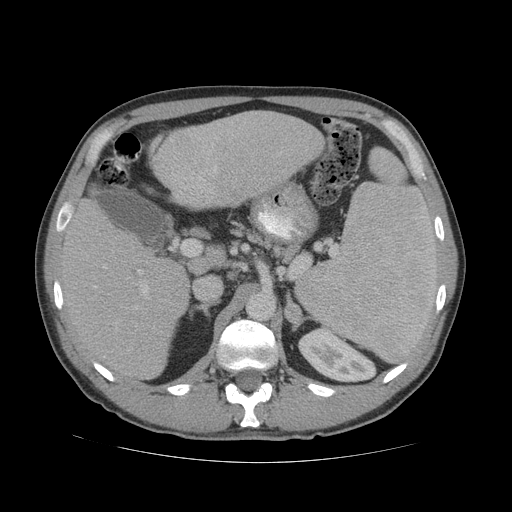
Contrast-enhanced abdominal CT (liver protocol), one axial slice; slice 35 of 81 in the series (ordered by position); reconstruction kernel STANDARD; 140 kVp; soft-tissue window (W 400 / L 40 HU); 2.5 mm slice thickness; 512 × 512 image matrix. Case-level facts recorded for this patient, not image findings: diagnosis: hepatocellular carcinoma (patient treated with transarterial chemoembolisation; whether this scan precedes or follows treatment is not stated here); TNM stage (as recorded): Stage-IVB; Child-Pugh class: B; tumour differentiation: well differentiated; tumour nodularity: multinodular.
Annotated regions visible in this slice (semi-automatic segmentation, software-assisted and operator-edited):
- liver parenchyma outside the tumour (the mass and vessels are separate outlines, so this box may not span the whole liver): bounding box <56,110,324,380> (left, top, right, bottom; pixels)
- liver vessels: <61,136,217,294>